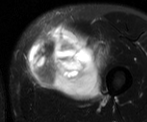
MRI of an extremity soft-tissue mass, one axial slice. Slice 22 of 52 in the series (ordered by position). T2-weighted fat-saturated. MR volume resampled by the dataset authors to the PET/CT grid (not the native acquisition matrix). 3.27 mm slice thickness. 147 × 122 image matrix, field of view 144 × 119 mm. Male patient. Case-level facts recorded for this patient, not image findings: histological type: pleiomorphic liposarcoma; grade: high; site of the primary tumour: left thigh.
Structures marked on this image (expert contour drawn on MRI and transferred to this co-registered scan by the dataset authors):
- gross tumour volume including surrounding oedema: bounding box (x1, y1, x2, y2) in pixels: (25, 21, 111, 100)
- gross tumour volume (mass): (27, 25, 102, 100)